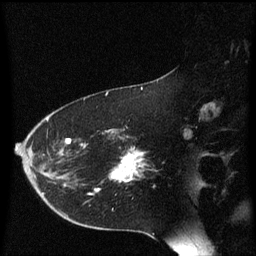
Breast MRI (dynamic contrast-enhanced), one sagittal slice. Slice 39 of 60 in the series (ordered by position). Dynamic contrast-enhanced series, image 2 of 3 at this slice position (ordered by acquisition). 1.5 T. TE 4.2 ms, TR 8.4 ms. 256 × 256 image matrix, field of view 200 × 200 mm. Patient: female, 54 years. From the clinical record (not read from this slice): setting: breast cancer imaged before/during neoadjuvant chemotherapy; receptor status: HR-positive, HER2-negative.
Annotated regions visible in this slice (semi-automatically segmented with operator editing):
- analysis volume of interest (the breast-tissue region the enhancement analysis was run in; not a lesion): bounding box [x1, y1, x2, y2] px = [102, 130, 146, 191]
- tumour enhancement mask (voxels above the 70 % enhancement threshold inside the analysis volume of interest): [113, 150, 146, 181]